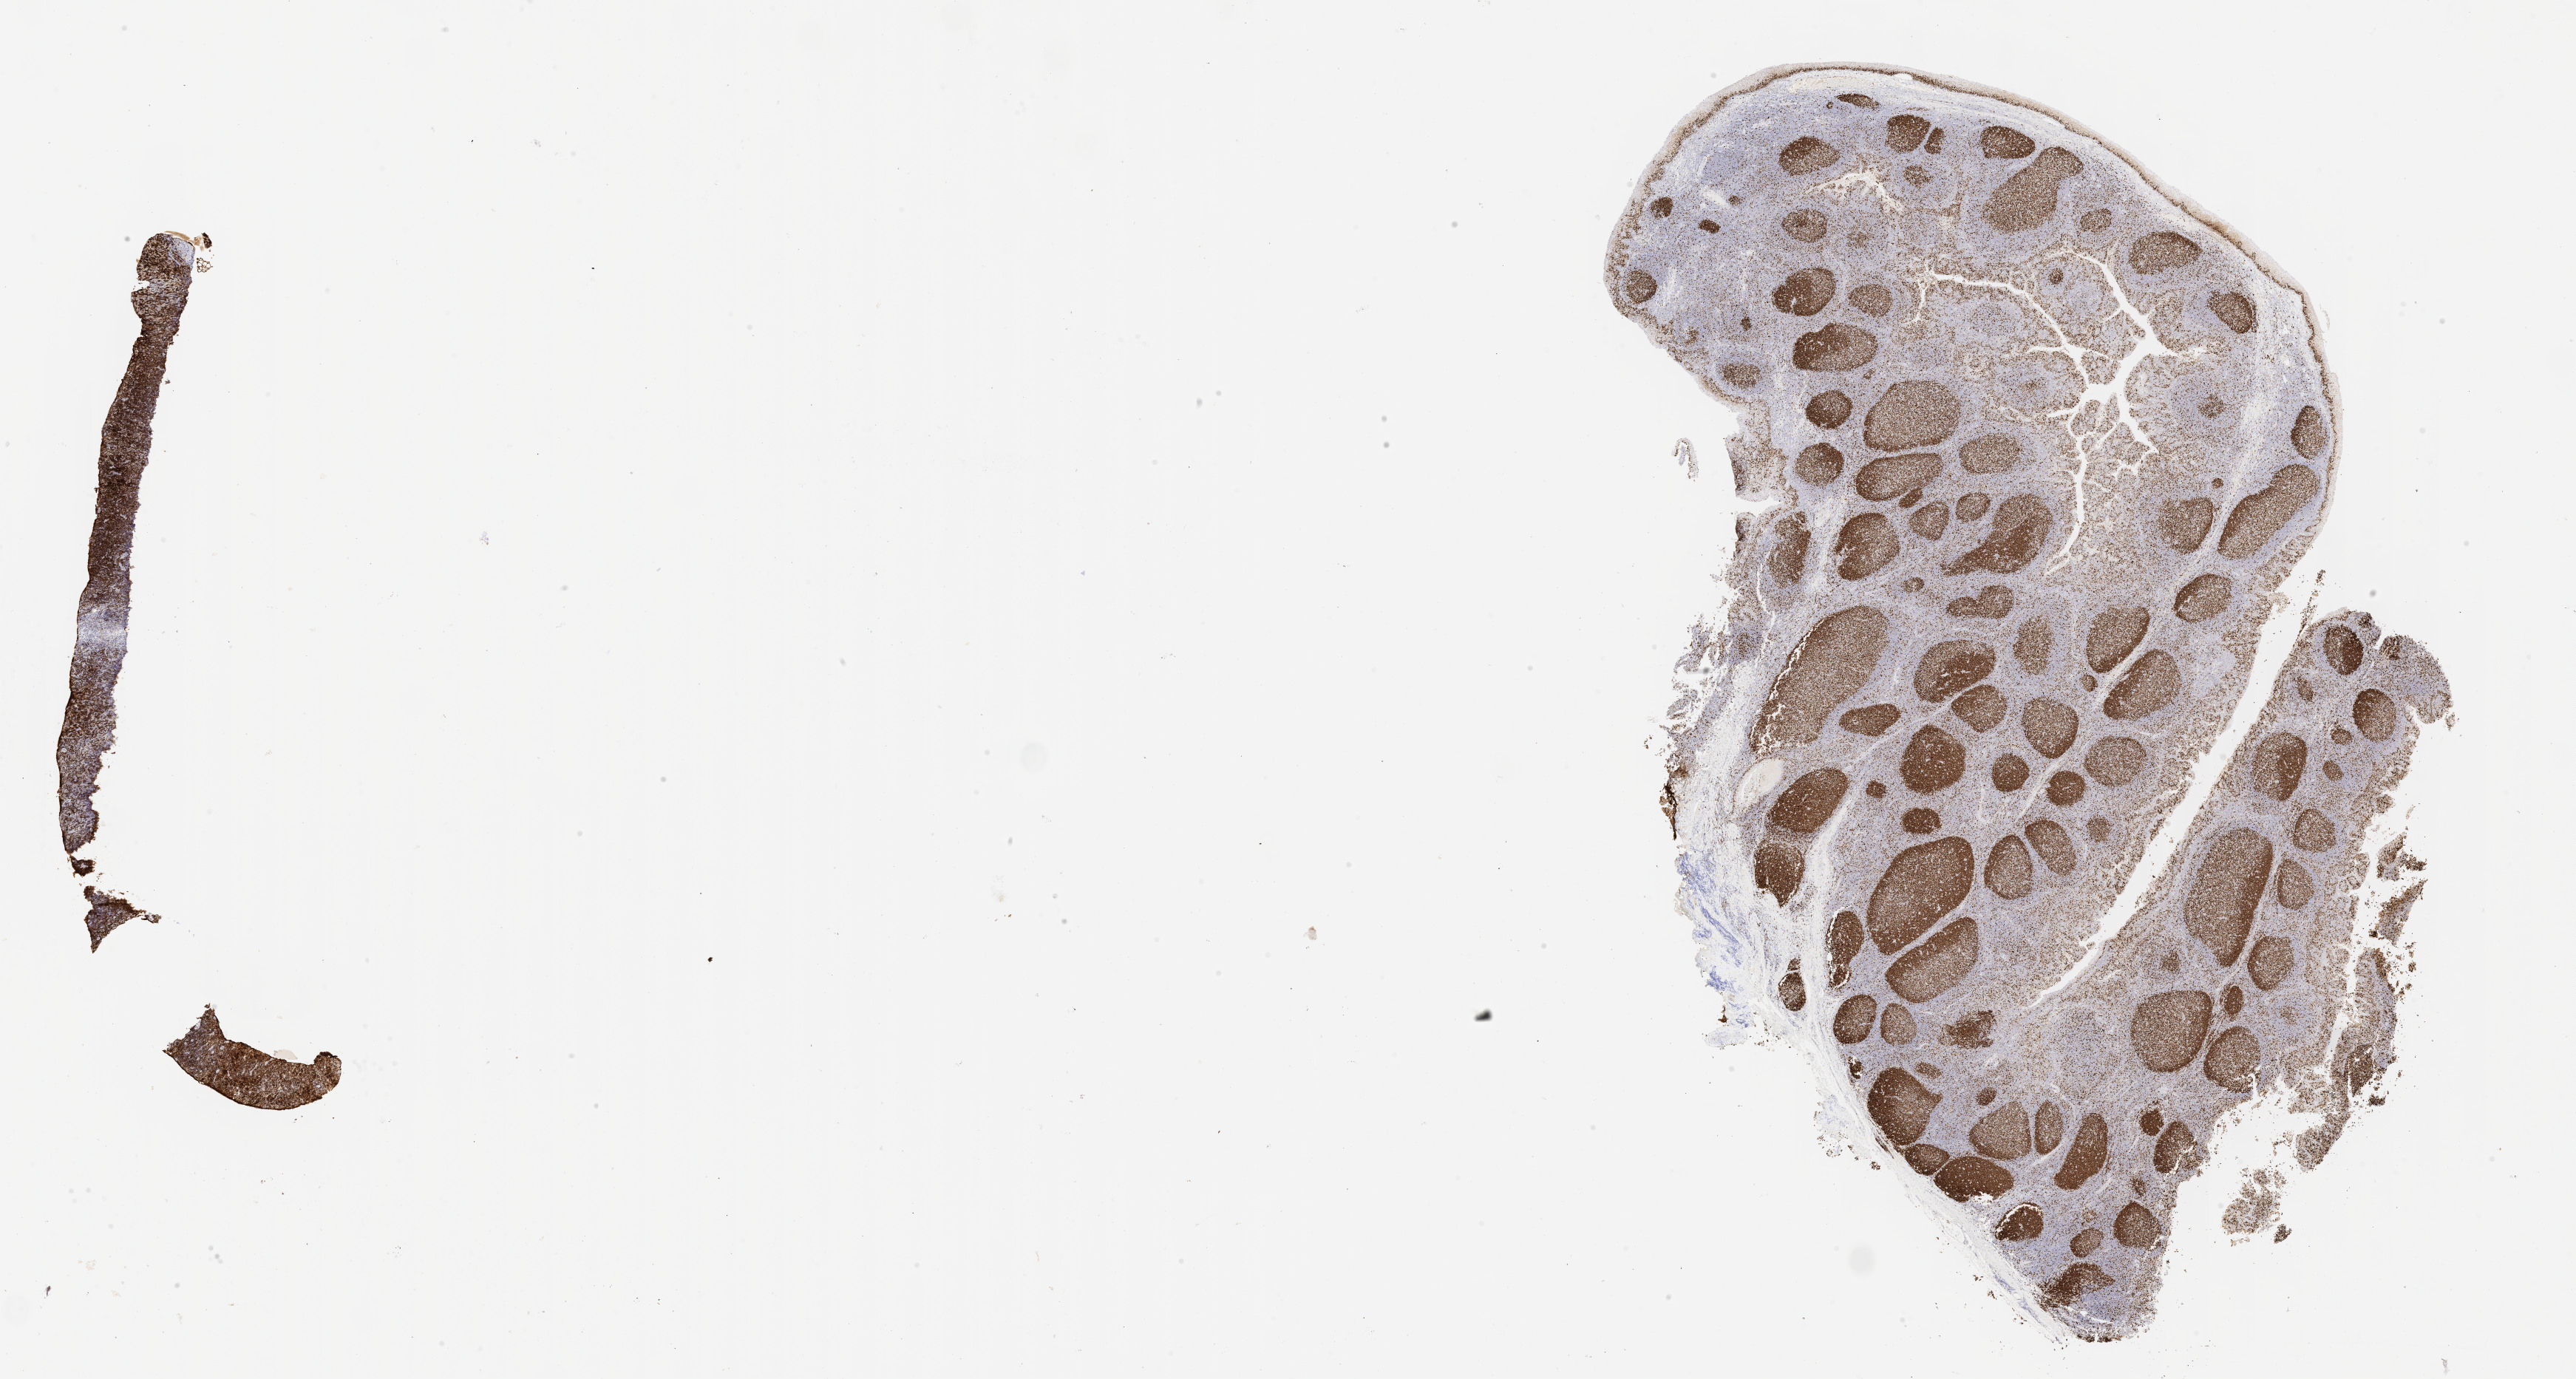
IHC for Ki-67, whole-slide image, whole scanned area (about 28.2 x 15.1 mm) shown as a low-resolution overview, tumor tissue, anatomic site: ovary. Female, age 9 years at initial diagnosis.
• diagnosis: Burkitt lymphoma, NOS